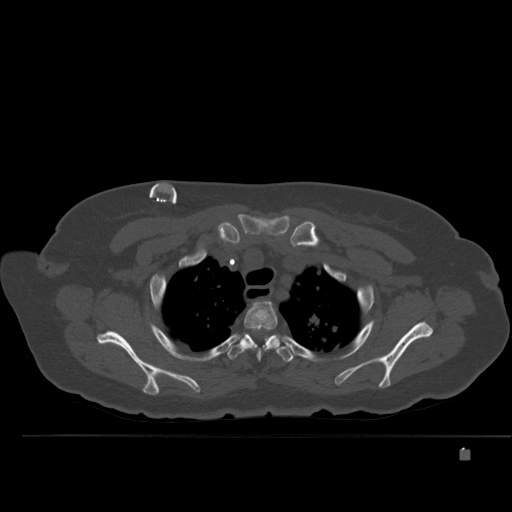
CT including the spine, one axial slice. Slice 386 of 477 in the series (ordered by position). Bone window (W 1800 / L 400 HU). 512 × 512 image matrix. Female patient, age 74 years. Case-level facts recorded for this patient, not image findings: primary cancer: colon.
Outlined on this slice (semi-automatic segmentation, software-assisted and operator-edited):
- T2 vertebra: bounding box [x1, y1, x2, y2] px = [238, 302, 279, 359]
- T3 vertebra: [227, 328, 294, 362]